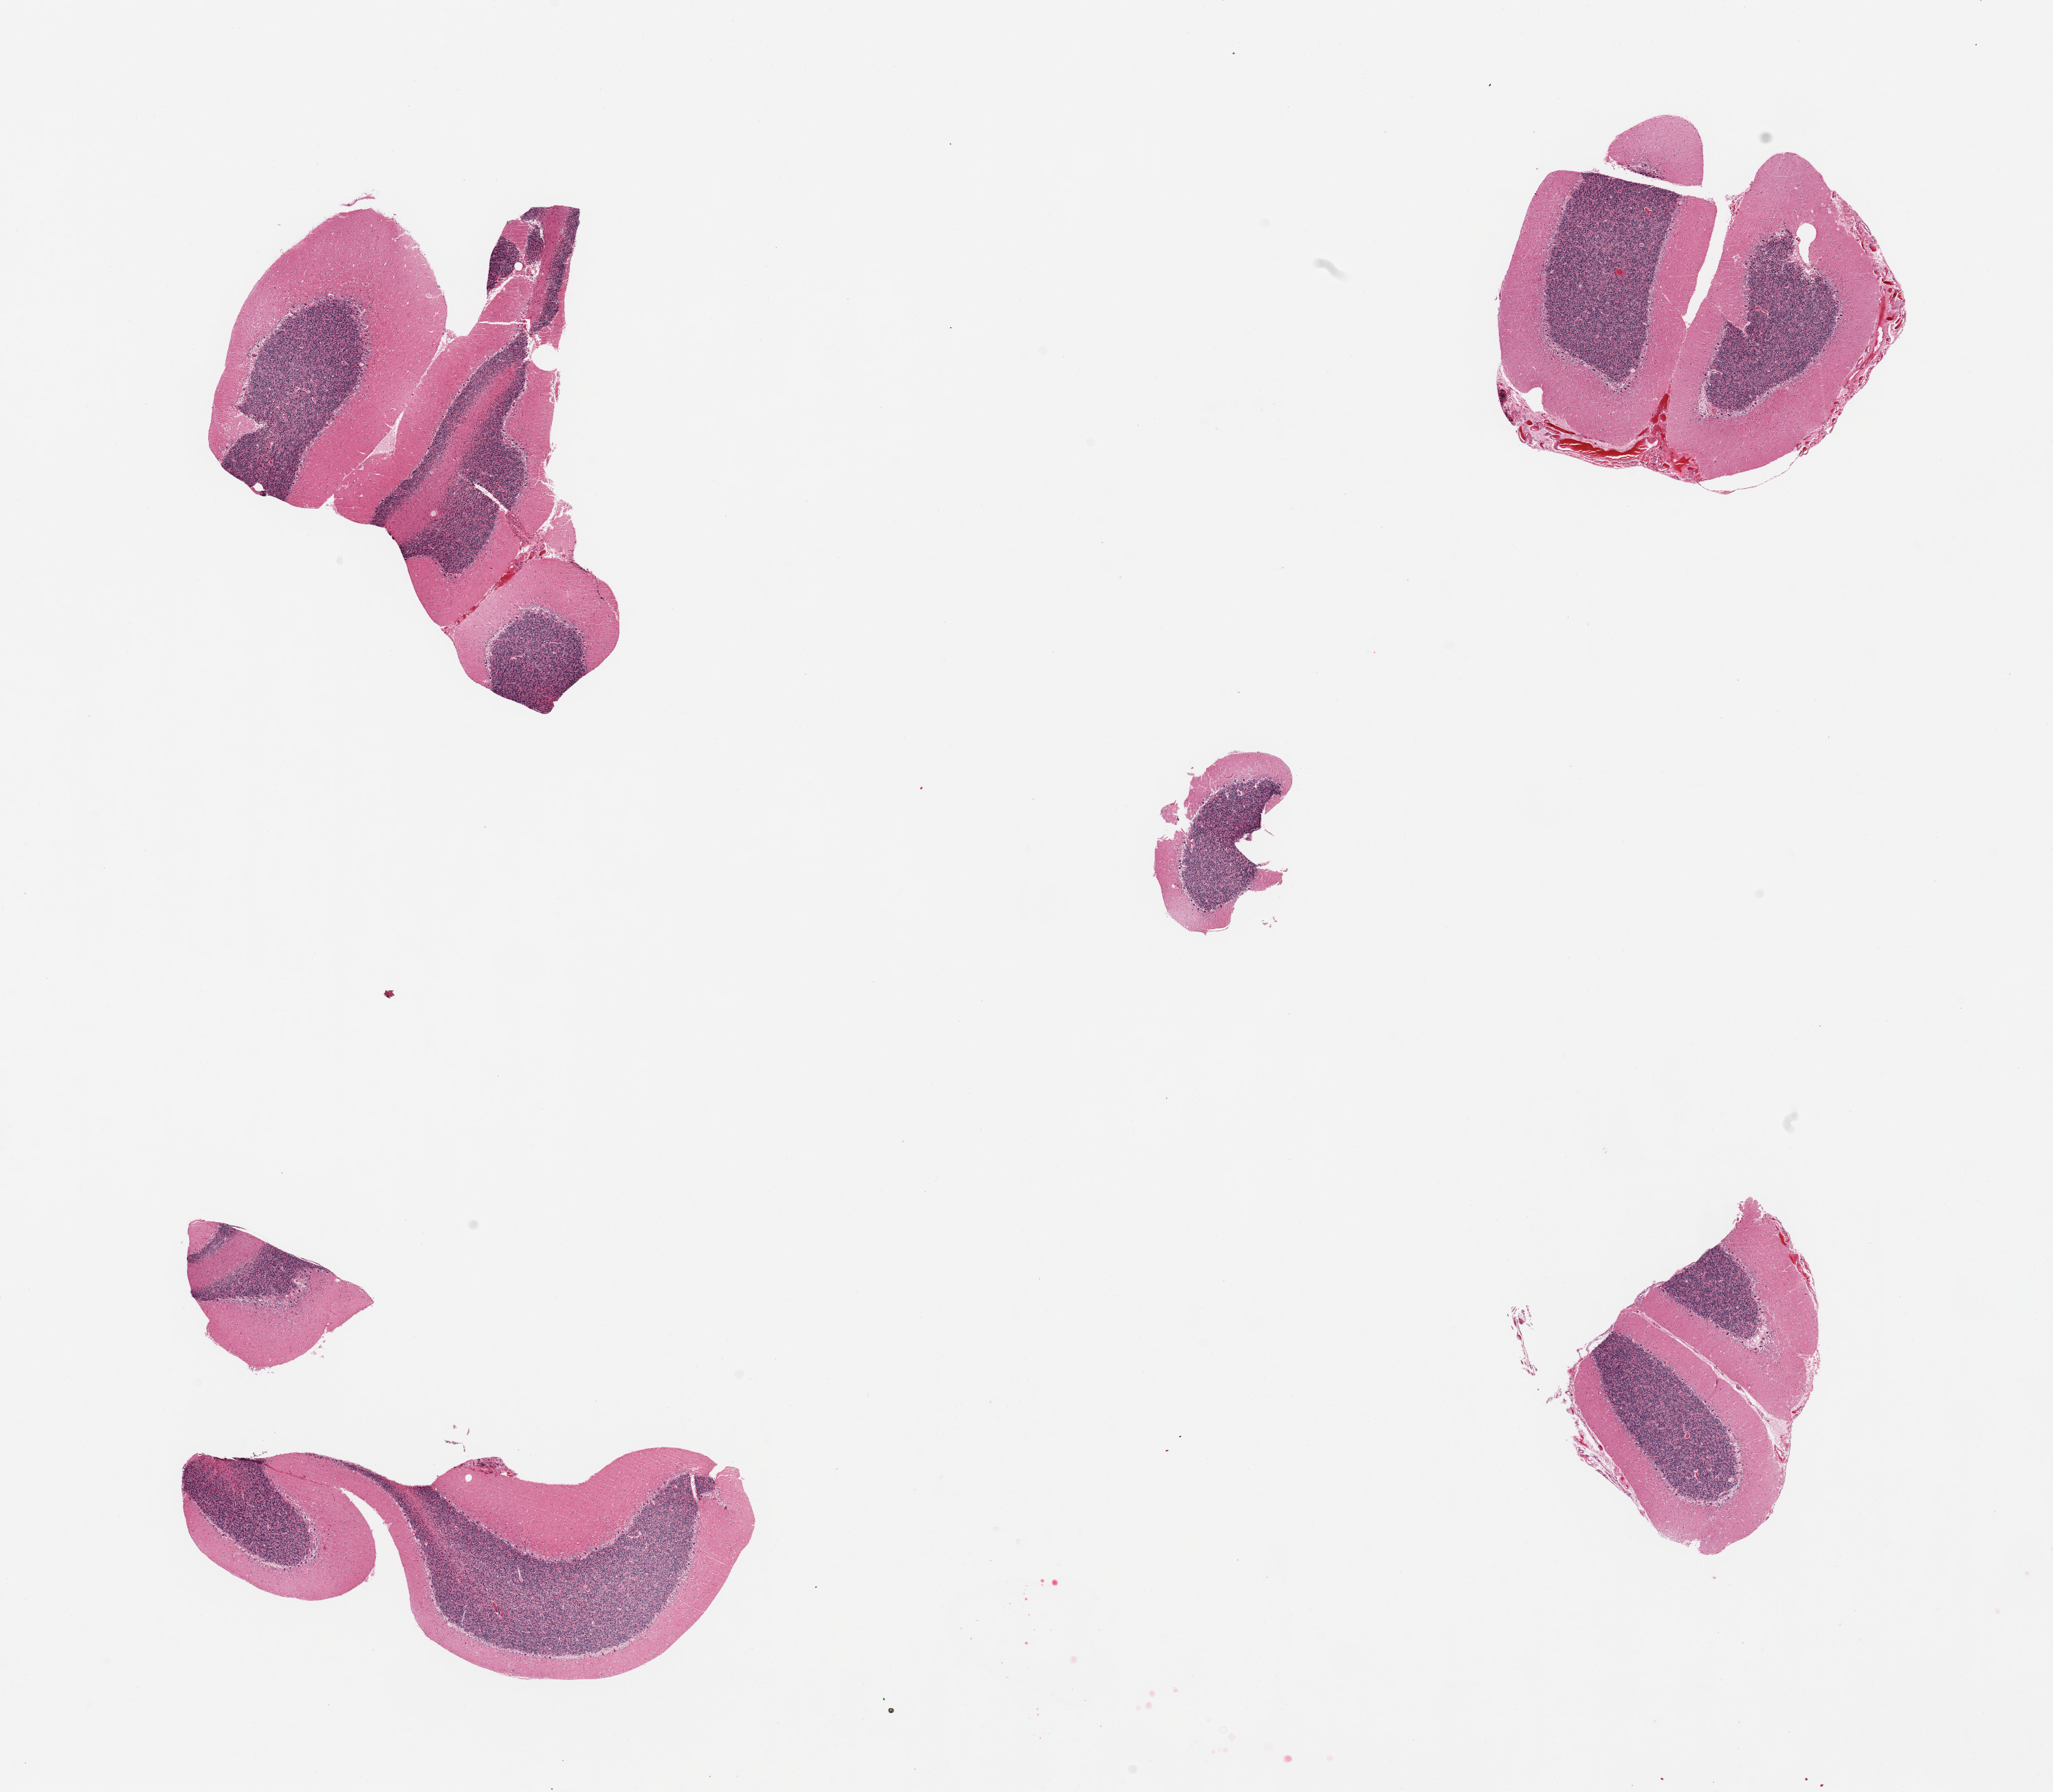
Digitized H&E-stained section — a low-resolution overview of the entire scanned area, about 23.6 x 20.6 mm (from a 20x scan); PAXgene-fixed paraffin-embedded (PFPE) section; target tissue: cerebellum; donor tissue sample. Donor: female.
Pathologist's review note for this sample: 4 pieces, no abnormalities.